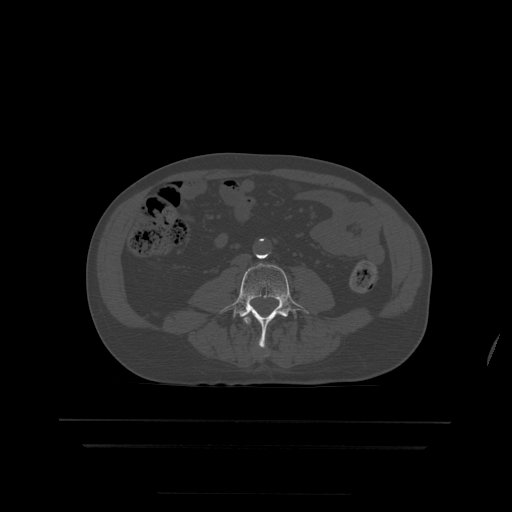
CT including the spine, one axial slice. Position 98 of 522 along the scan axis. Bone window (W 1800 / L 400 HU). 1.25 mm slice thickness. 512 × 512 image matrix, field of view 436 × 436 mm. Patient age 68 years. Case-level facts recorded for this patient, not image findings: primary cancer: urothelial.
Outlined on this slice (semi-automatically segmented with operator editing):
- L3 vertebra: bounding box <243,317,267,348> (left, top, right, bottom; pixels)
- L4 vertebra: <220,264,309,348>